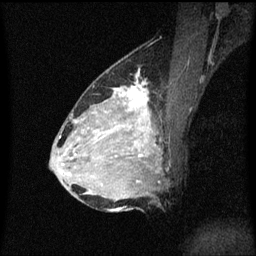
Breast MRI (dynamic contrast-enhanced), one sagittal slice; slice 33 of 60 in the series (ordered by position); dynamic contrast-enhanced series, image 2 of 3 at this slice position (ordered by acquisition); 1.5 T; TE 4.2 ms, TR 8.4 ms; 256 × 256 image matrix, field of view 200 × 200 mm. Patient: female, 34 years. Case-level facts recorded for this patient, not image findings: setting: breast cancer imaged before/during neoadjuvant chemotherapy; receptor status: HR-positive, HER2-negative.
Outlined on this slice (semi-automatically segmented with operator editing):
- analysis volume of interest (the breast-tissue region the enhancement analysis was run in; not a lesion): bounding box [x1, y1, x2, y2] px = [69, 70, 171, 209]
- tumour enhancement mask (voxels above the 70 % enhancement threshold inside the analysis volume of interest): [74, 84, 155, 183]